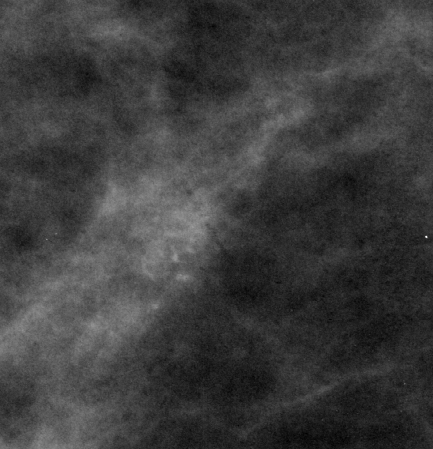
Region of interest cut from a scanned film mammogram (one marked finding), right breast, CC view, BI-RADS breast density category 2 (scale 1–4).
Finding: calcifications, morphology pleomorphic, distribution clustered; BI-RADS assessment category 4; pathology (as recorded): malignant.